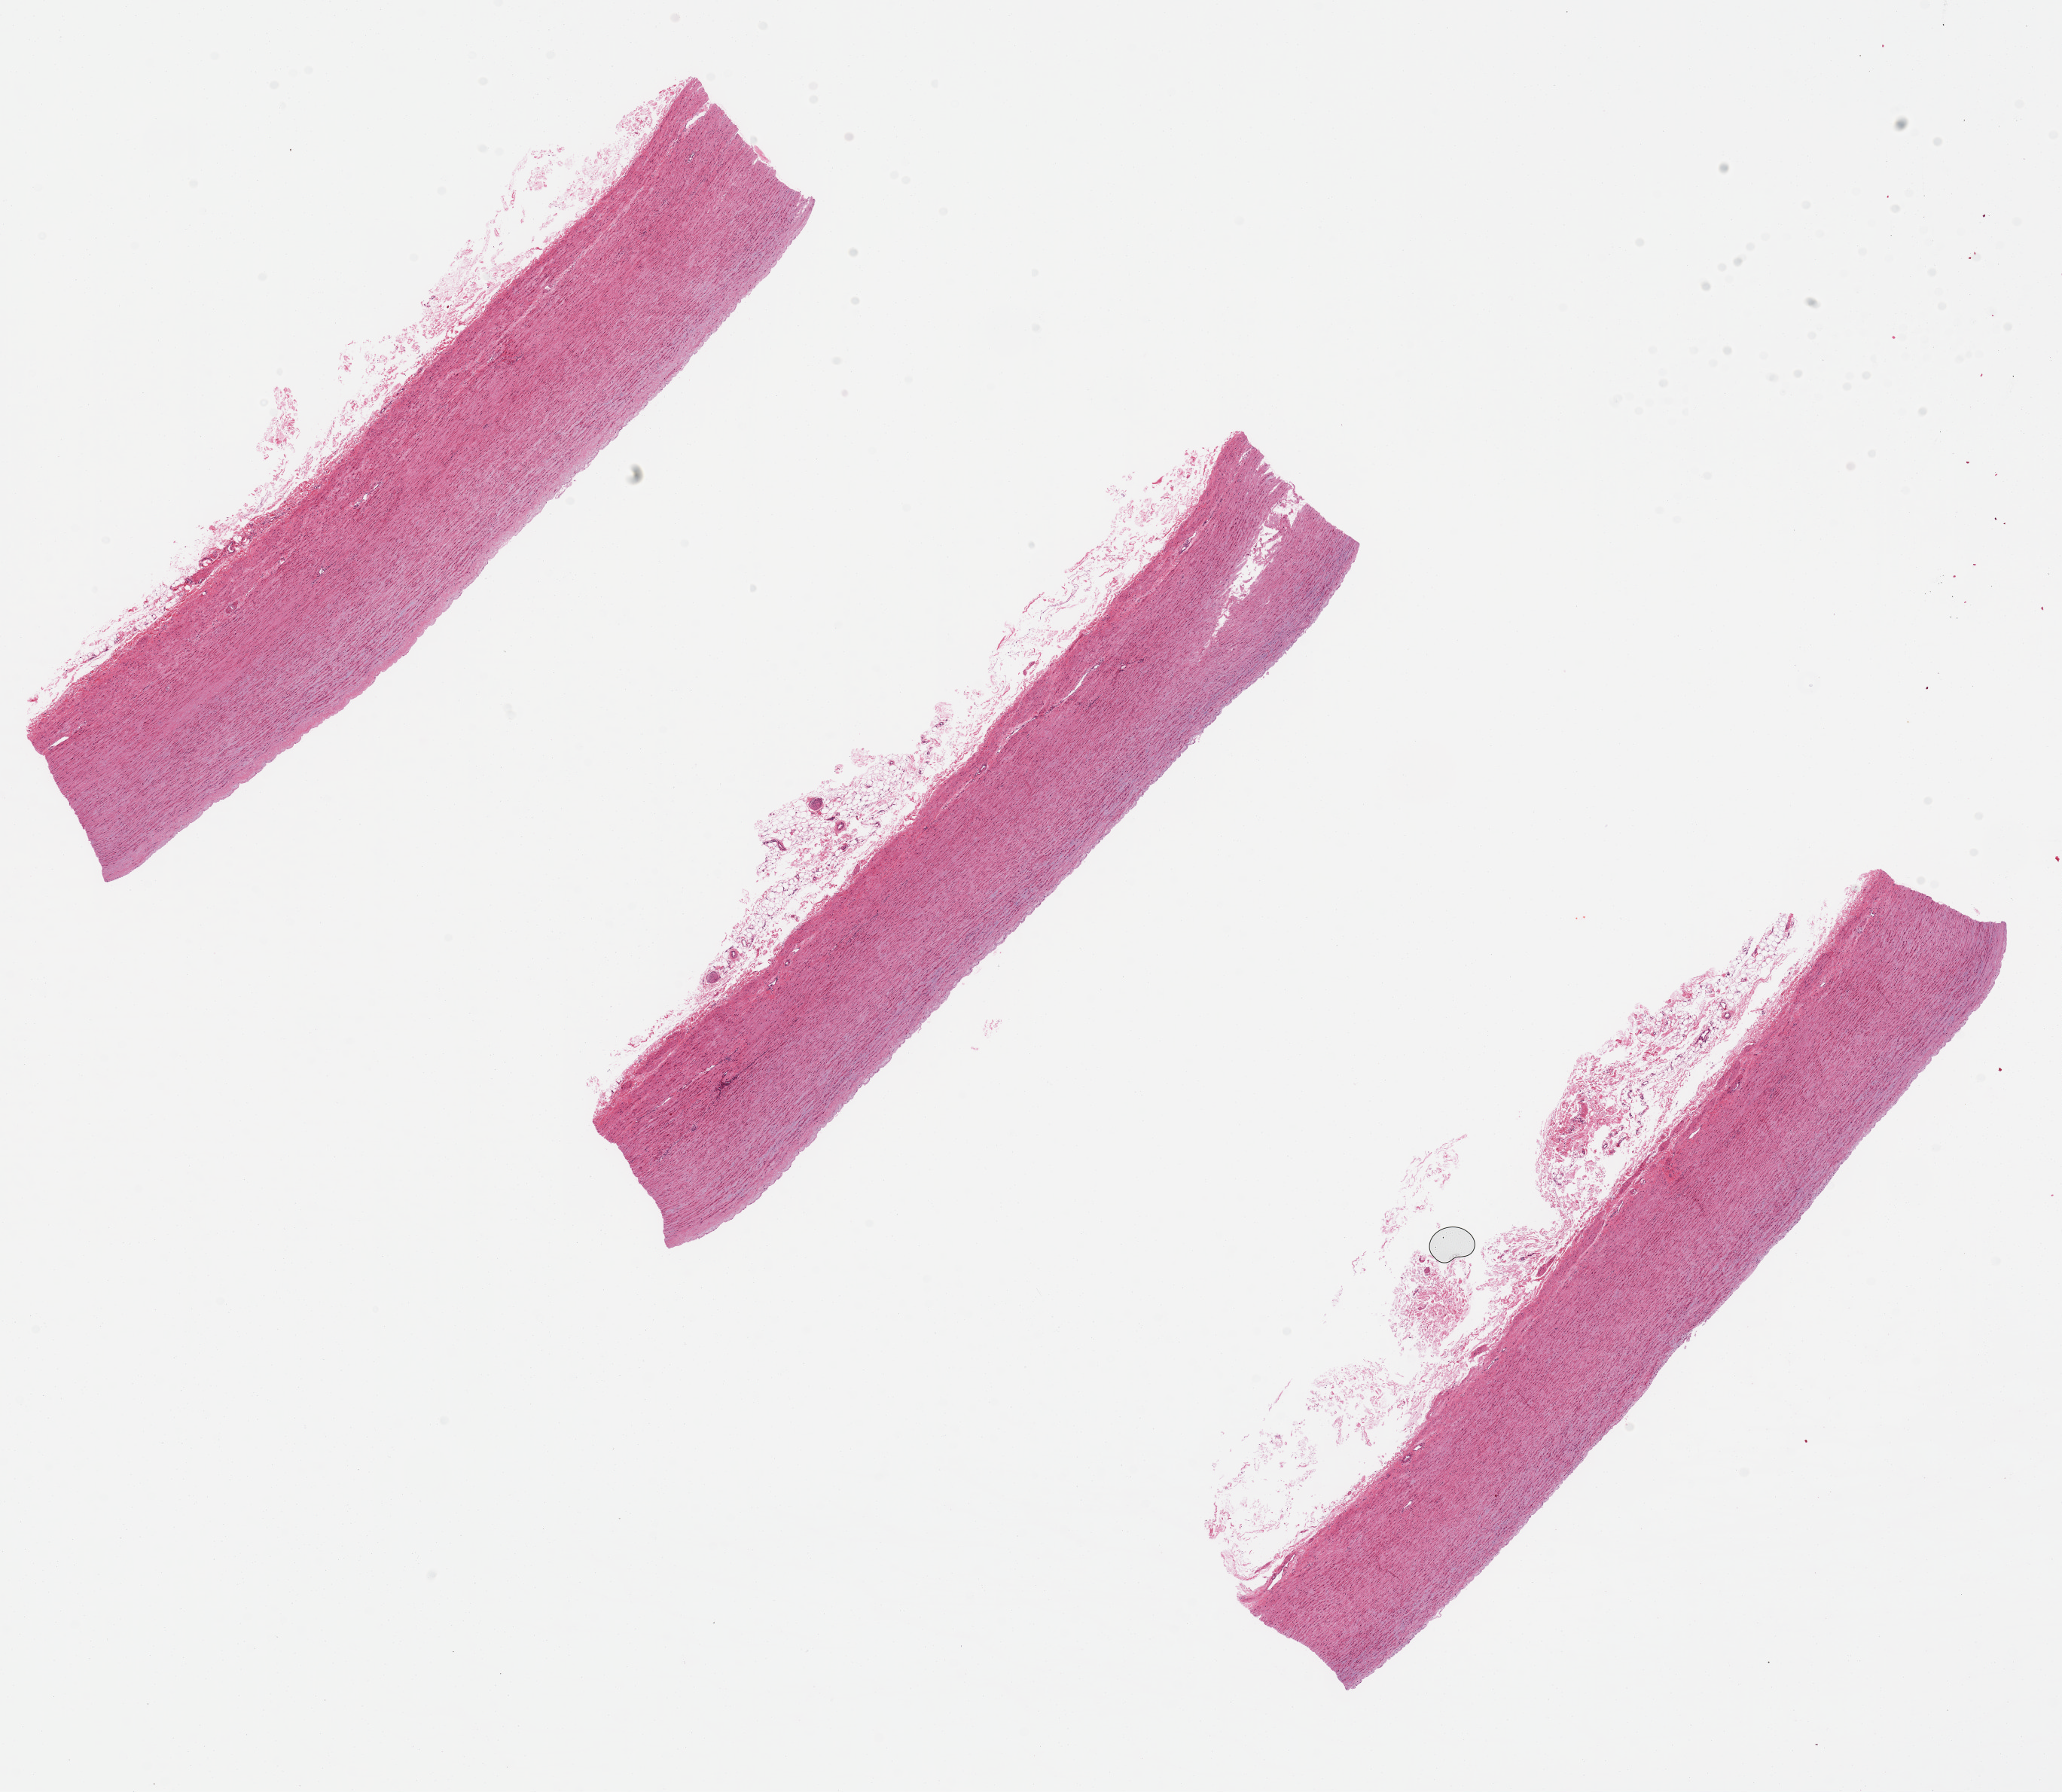
Digitized H&E-stained section, brightfield, a low-resolution overview of the entire scanned area, about 21.7 x 18.8 mm. PAXgene-fixed, paraffin-embedded tissue. Sampled site (target tissue): aorta. Donor tissue sample. Donor sex: male.
• review note (as recorded): minimal atherosclerosis. Vessel wall is ~75% of thickness